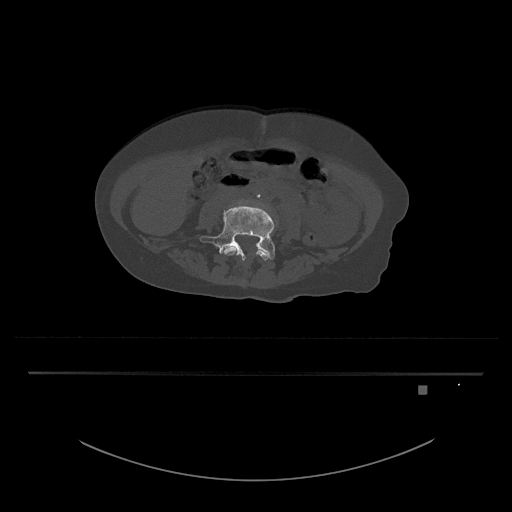
CT including the spine, one axial slice. Slice 323 of 797 in the series (ordered by position). Reconstruction kernel Br40s/3. Bone window (W 1800 / L 400 HU). 512 × 512 image matrix. Patient: female, 57 years. Case-level facts recorded for this patient, not image findings: primary cancer: cervical.
Annotated regions visible in this slice (semi-automatic segmentation, software-assisted and operator-edited):
- L4 vertebra: box from (x=224, y=246) to (x=271, y=260) px